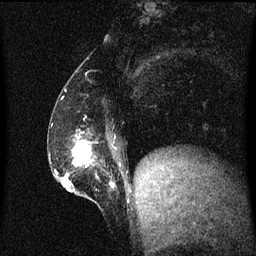
Breast MRI (dynamic contrast-enhanced), one sagittal slice; slice 21 of 60 in the series (ordered by position); dynamic contrast-enhanced series, image 2 of 3 at this slice position (ordered by acquisition); 1.5 T; TE 4.2 ms, TR 8.4 ms; 2 mm slice thickness; 256 × 256 image matrix. Female patient, age 52 years. From the clinical record (not read from this slice): setting: breast cancer imaged before/during neoadjuvant chemotherapy; receptor status: HER2-positive.
Annotated regions visible in this slice (semi-automatic segmentation, software-assisted and operator-edited):
- analysis volume of interest (the breast-tissue region the enhancement analysis was run in; not a lesion): bounding box [x1, y1, x2, y2] px = [62, 132, 117, 203]
- tumour enhancement mask (voxels above the 70 % enhancement threshold inside the analysis volume of interest): [66, 142, 115, 187]